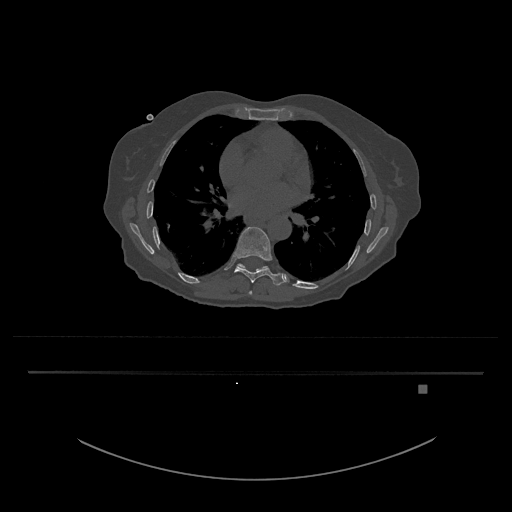
CT including the spine, one axial slice; position 754 of 797 along the scan axis; bone window (W 1800 / L 400 HU); 0.5 mm slice thickness; 512 × 512 image matrix, field of view 500 × 500 mm. Patient: female, 57 years. Case-level facts recorded for this patient, not image findings: primary cancer: cervical.
Annotated regions visible in this slice (semi-automatically segmented with operator editing):
- T10 vertebra: bounding box (x1, y1, x2, y2) in pixels: (237, 263, 269, 272)
- T8 vertebra: (249, 291, 252, 295)
- T9 vertebra: (235, 226, 284, 286)